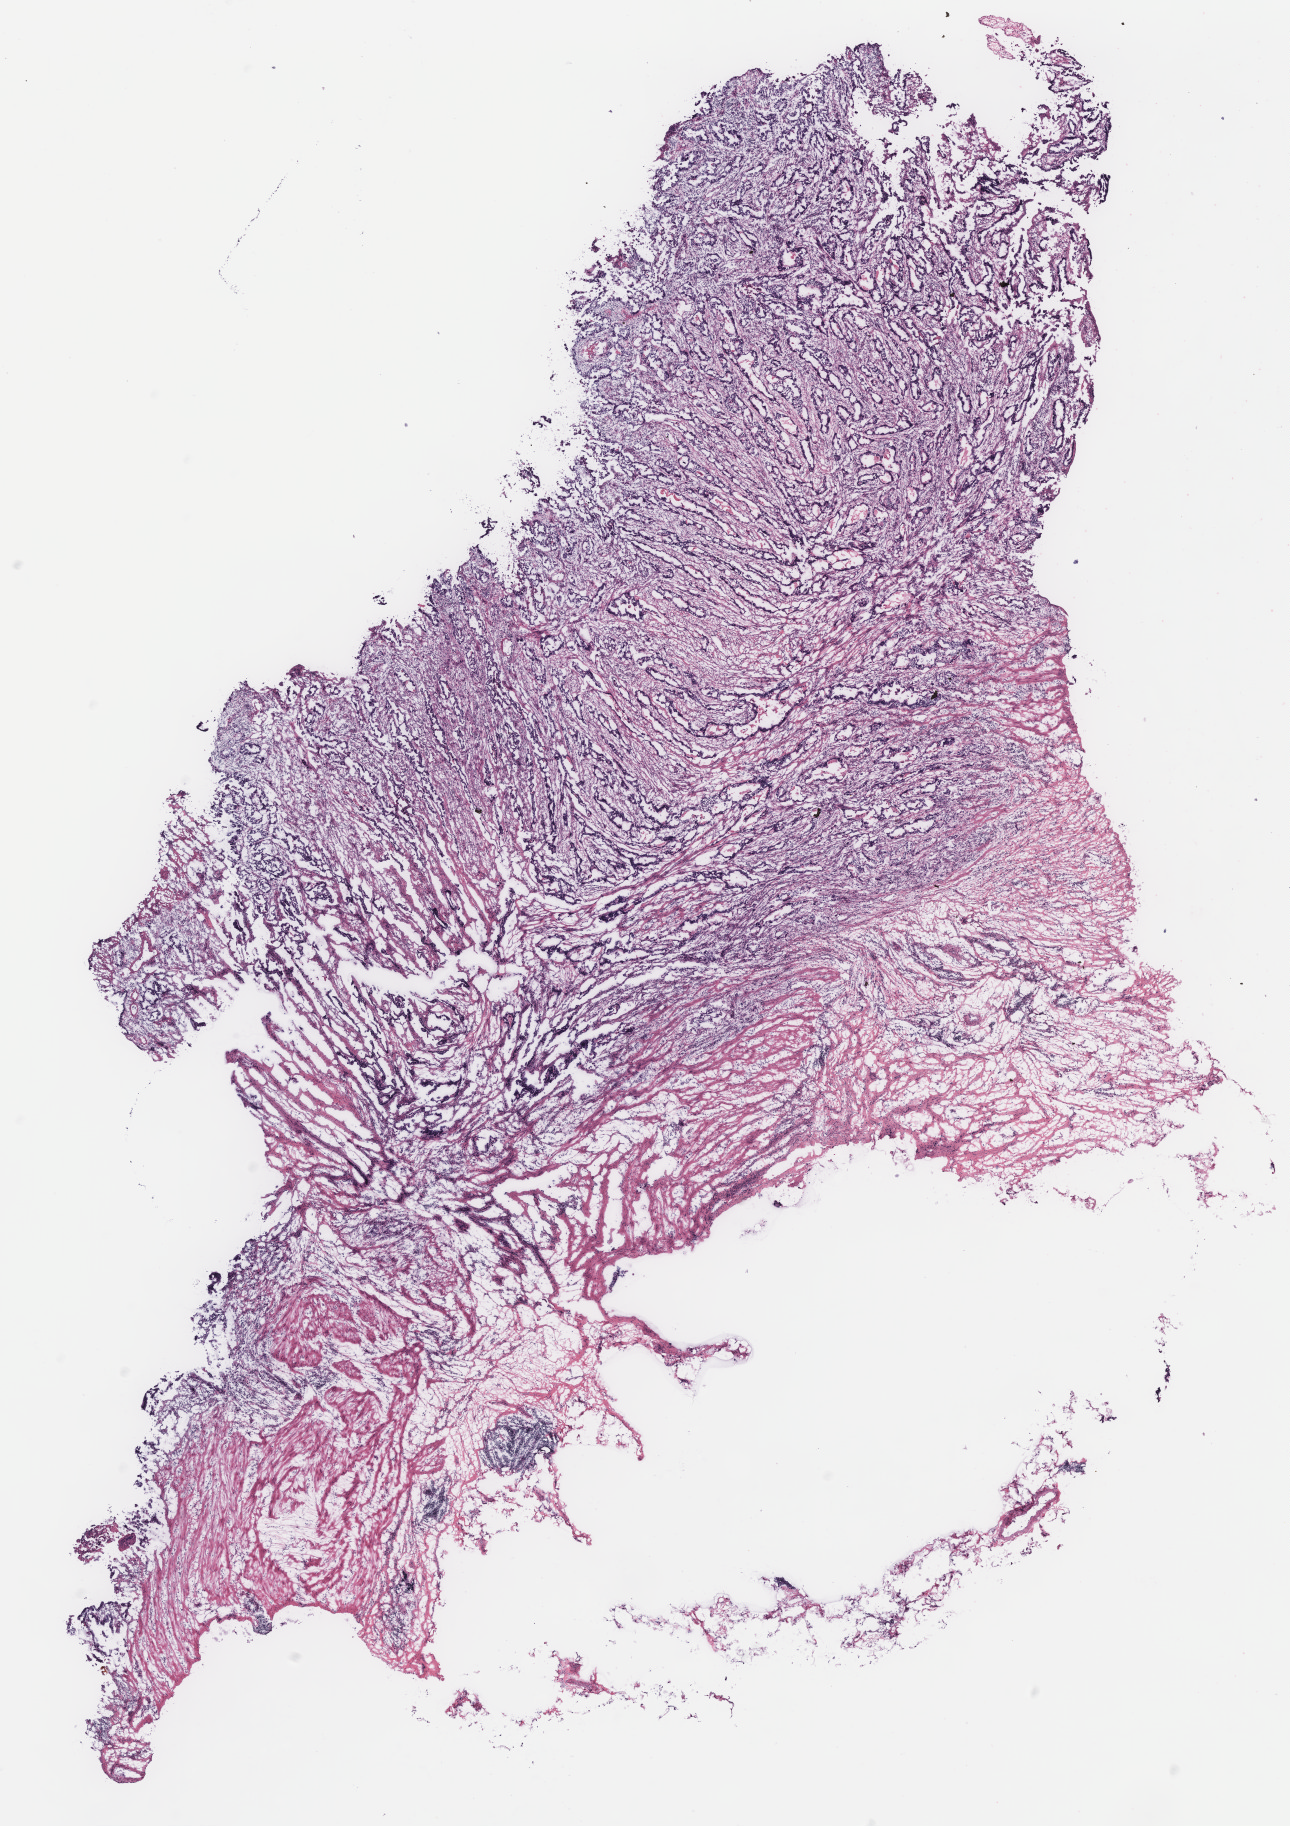
Whole-slide histology image, H&E — shown as a low-resolution overview of the whole scanned area (about 10.3 x 14.6 mm), colon, tissue type not recorded. Female patient.
Patient diagnosis: Adenocarcinoma, NOS.